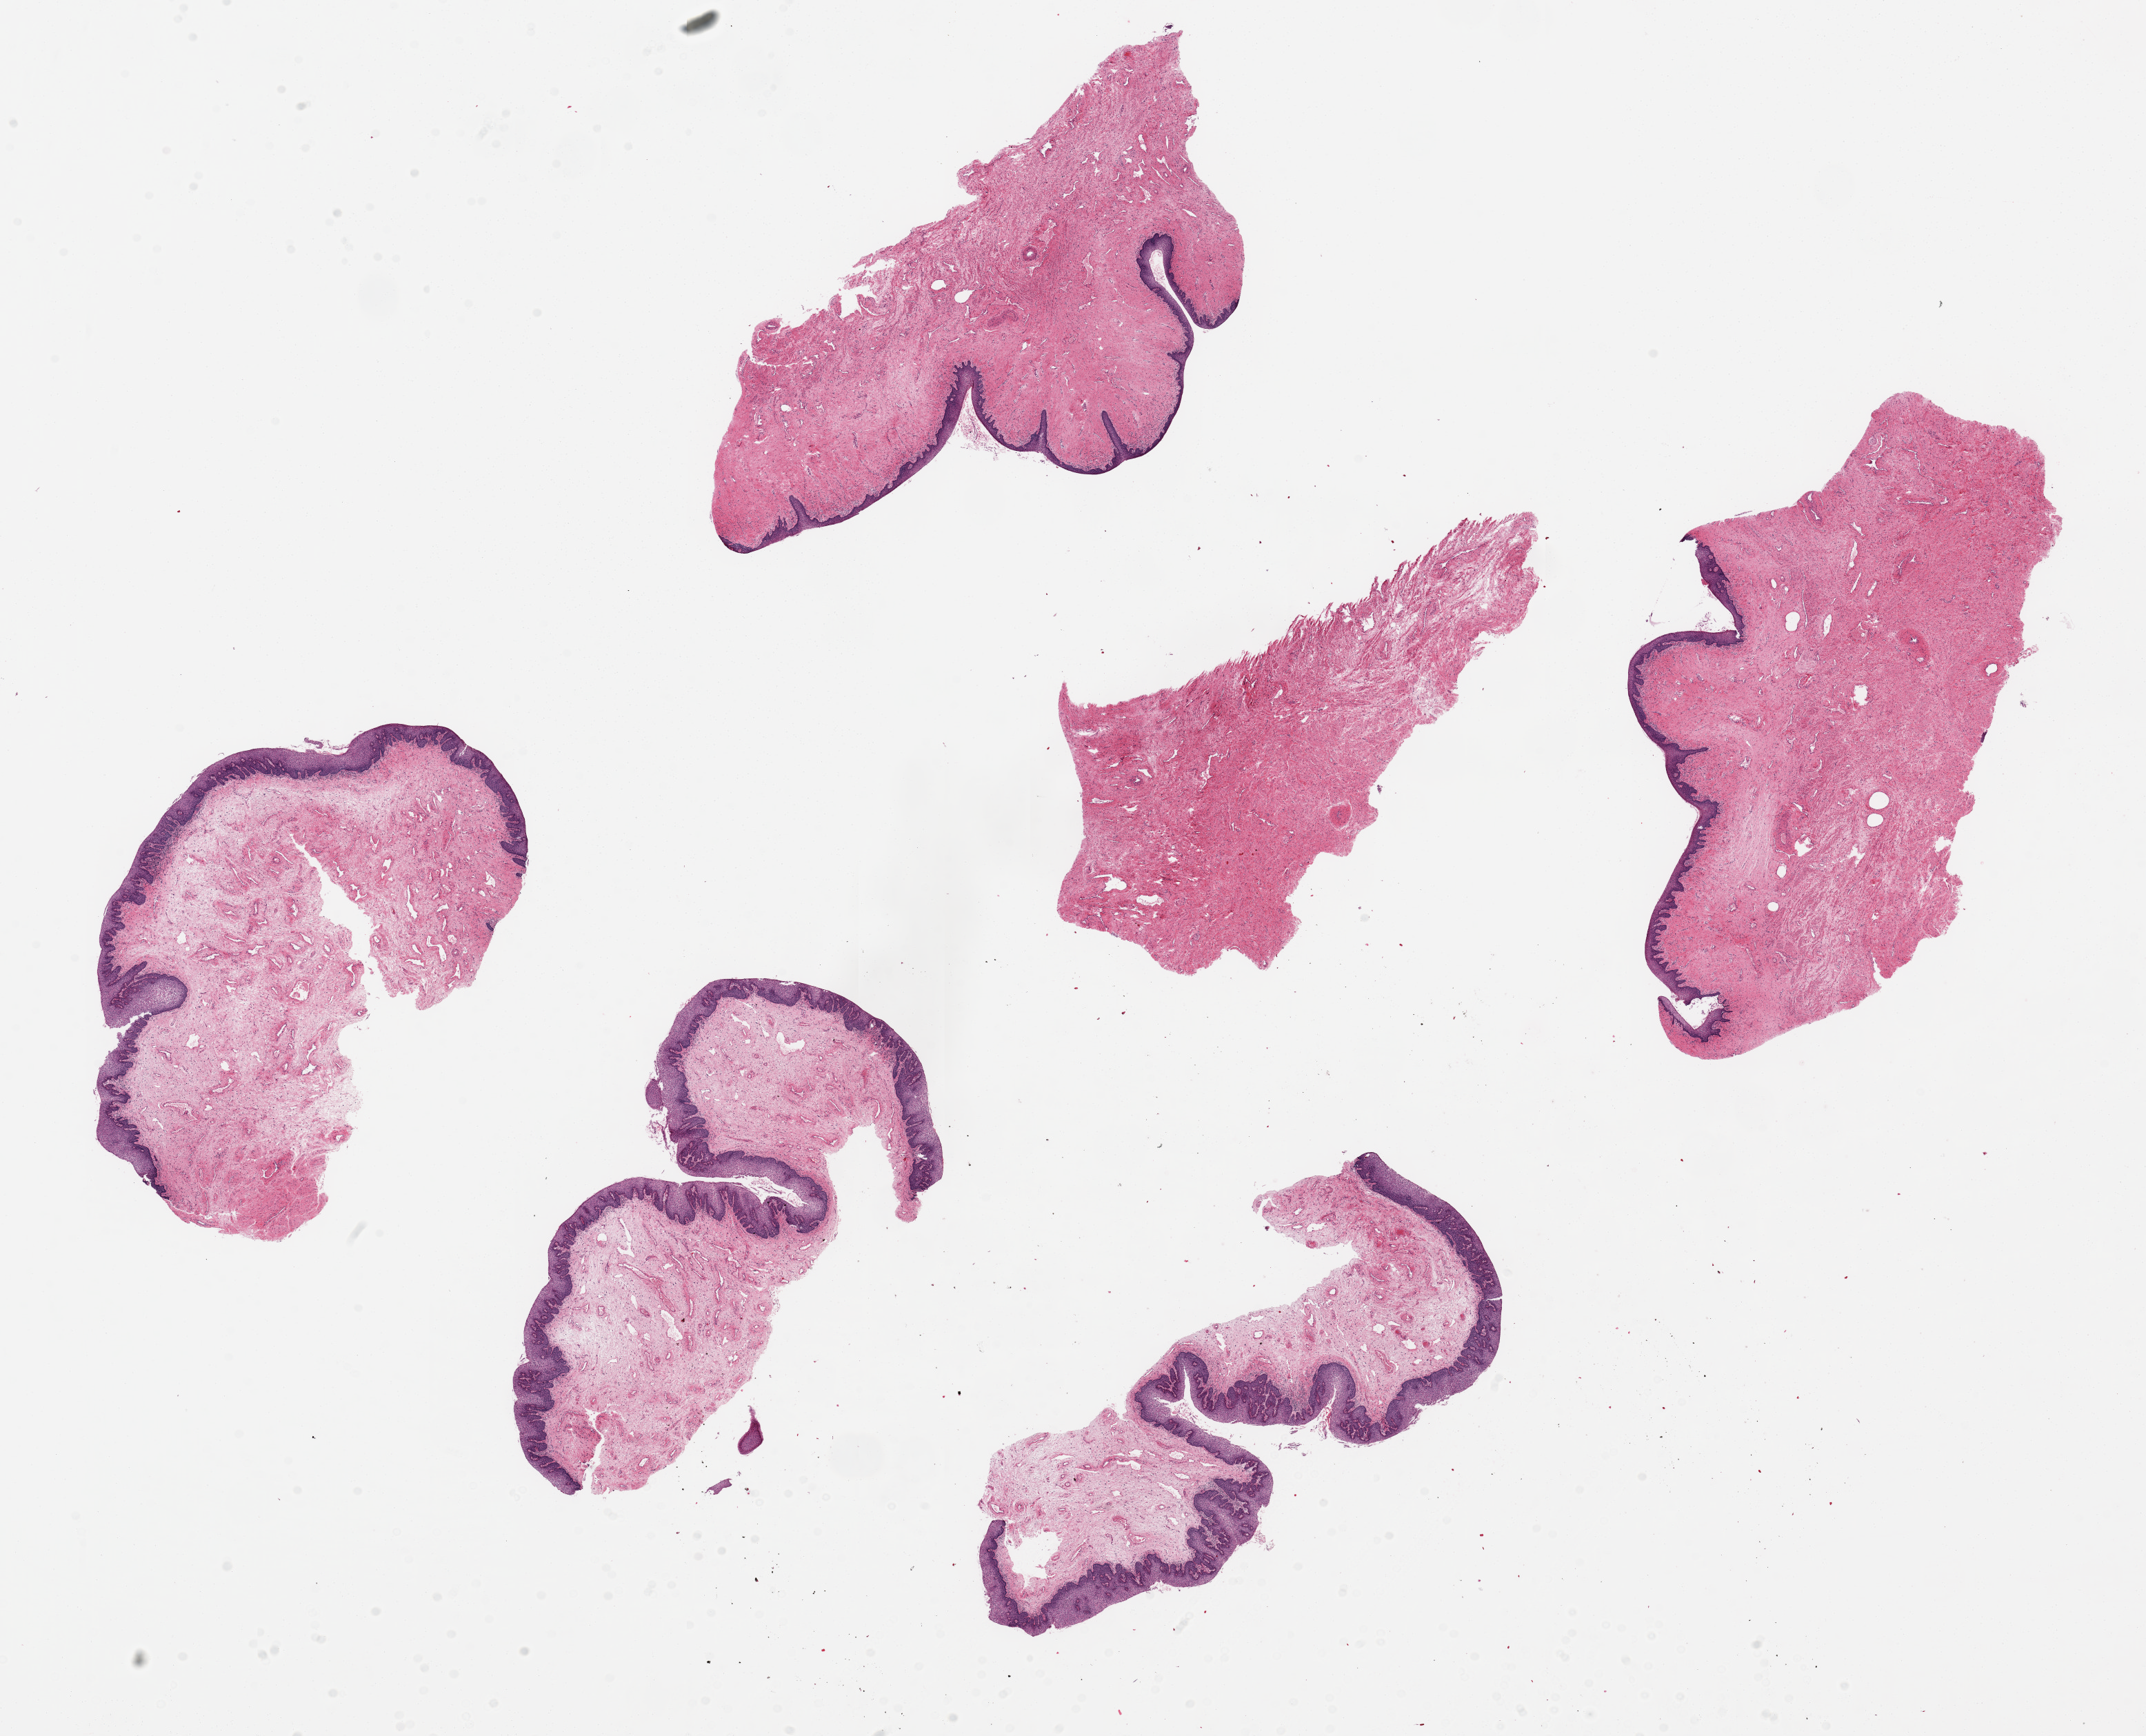
Digitized H&E-stained section, low-resolution overview of the scanned area, about 24.6 x 19.9 mm (slide scanned at 20x); PAXgene-fixed paraffin-embedded (PFPE) section; target tissue: vagina; donor tissue sample. Donor sex: female.
Review note (as recorded): 6 ~6x2.5mm pieces; squamous mucosa is ~10 thickness/ r/o dysplasia on glass.